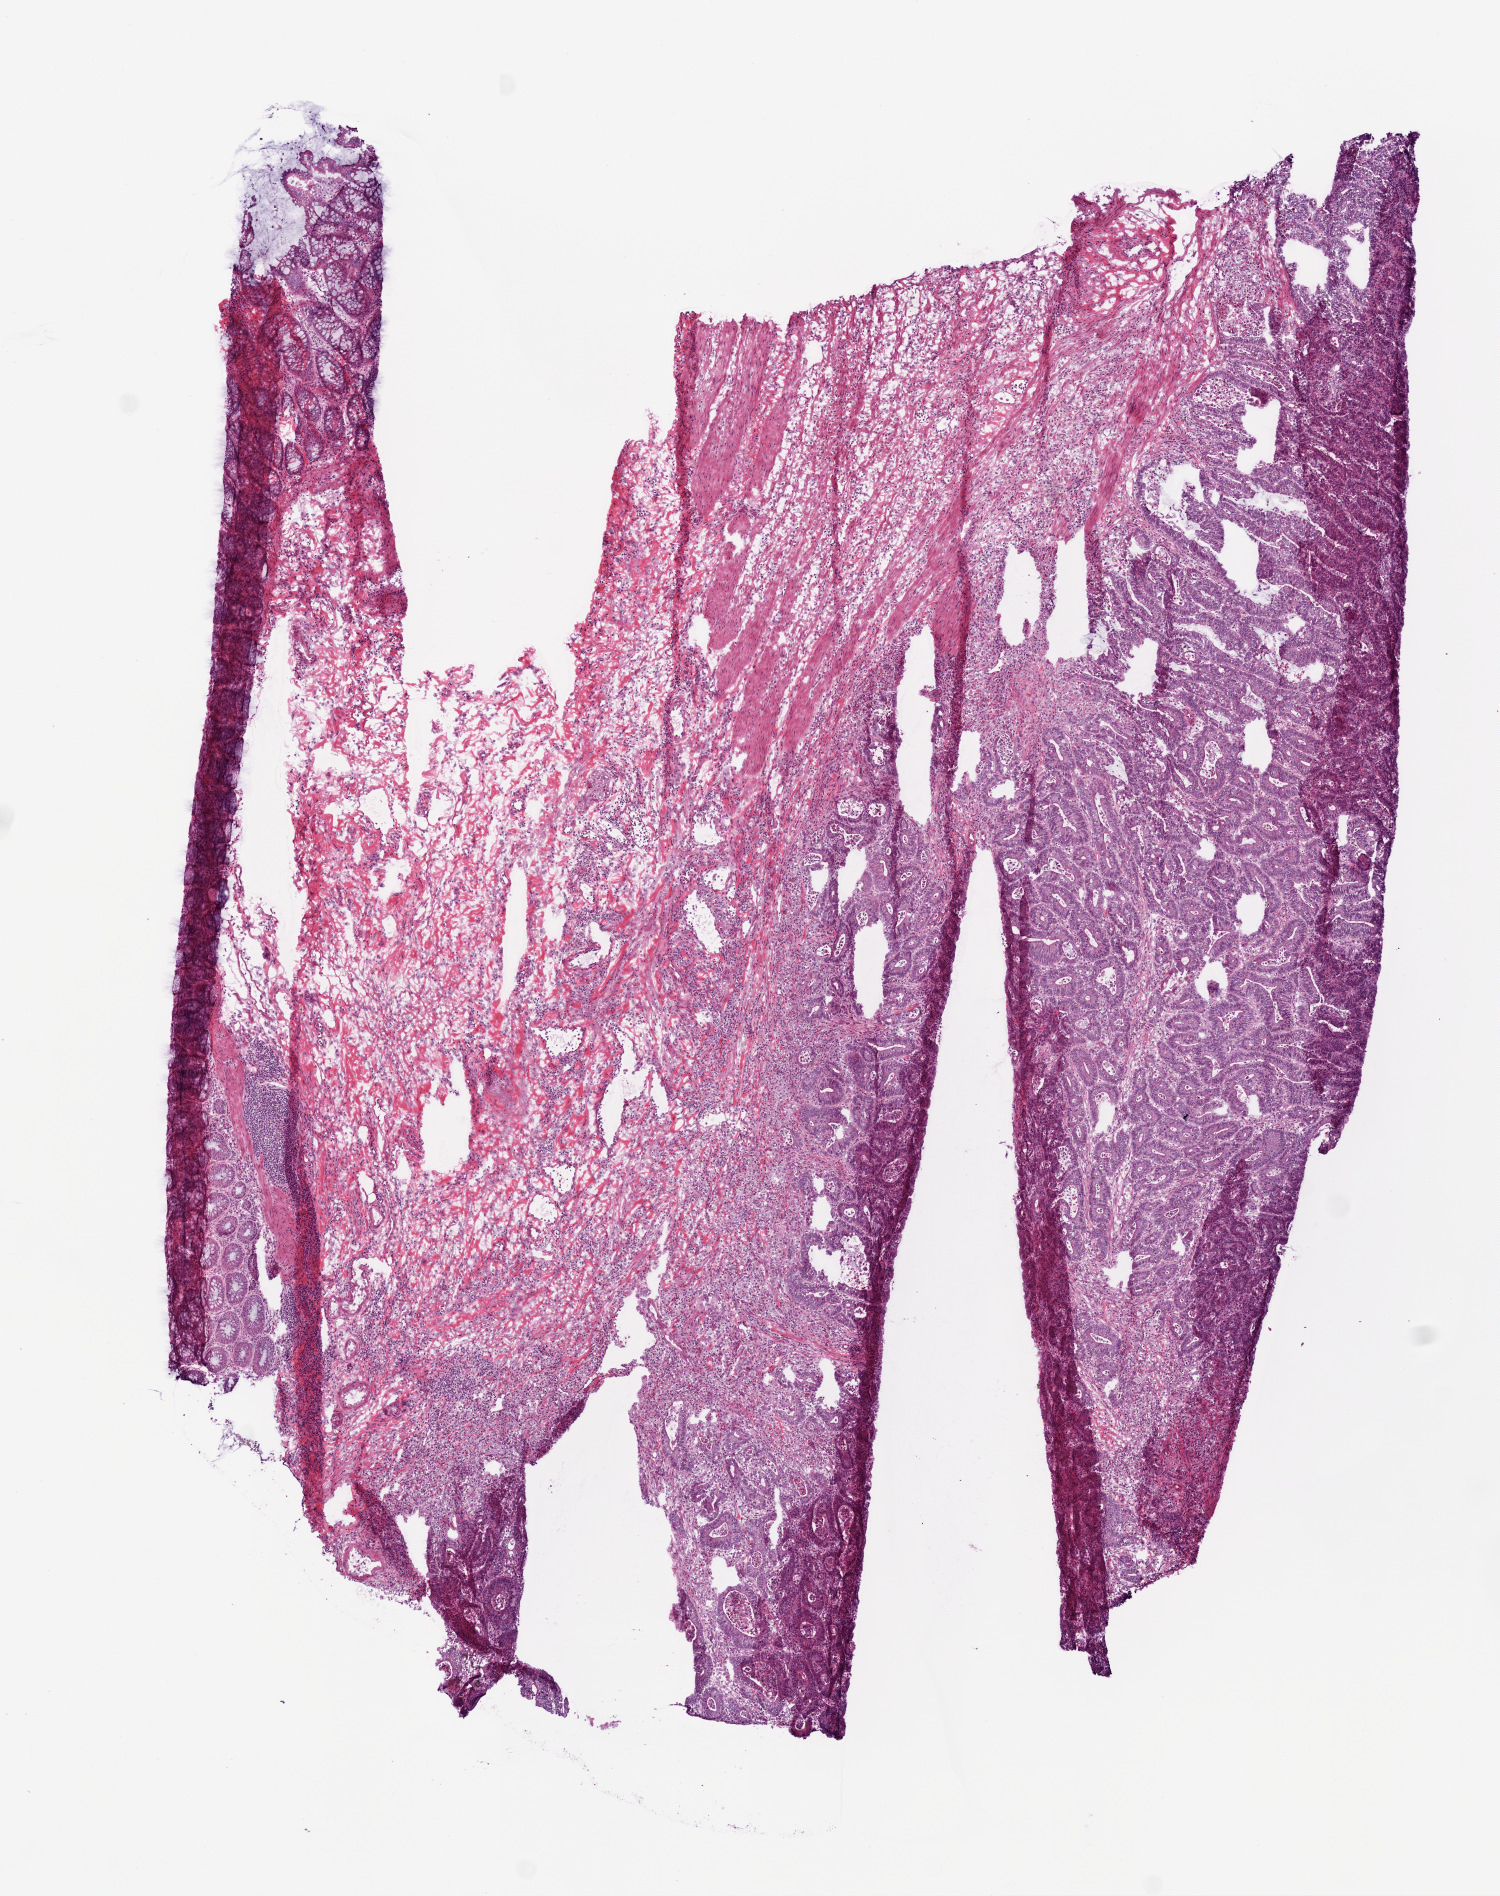
Digitized H&E-stained tissue section (whole slide) — whole scanned area (about 6.0 x 7.6 mm, acquisition: 20x scan) shown as a low-resolution overview, frozen section from the top of the tissue portion, sample: primary tumour, colon. Male, age 82 years at initial diagnosis. Composition of this section per pathologist review: tumour cells 48%, tumour nuclei 70%, normal cells 40%, stromal cells 10%, necrosis 2%.
* lymph nodes positive (case pathology): 0 of 16 examined
* pathologic diagnosis: Adenocarcinoma, NOS
* AJCC pathologic stage: IIA (6th edition)